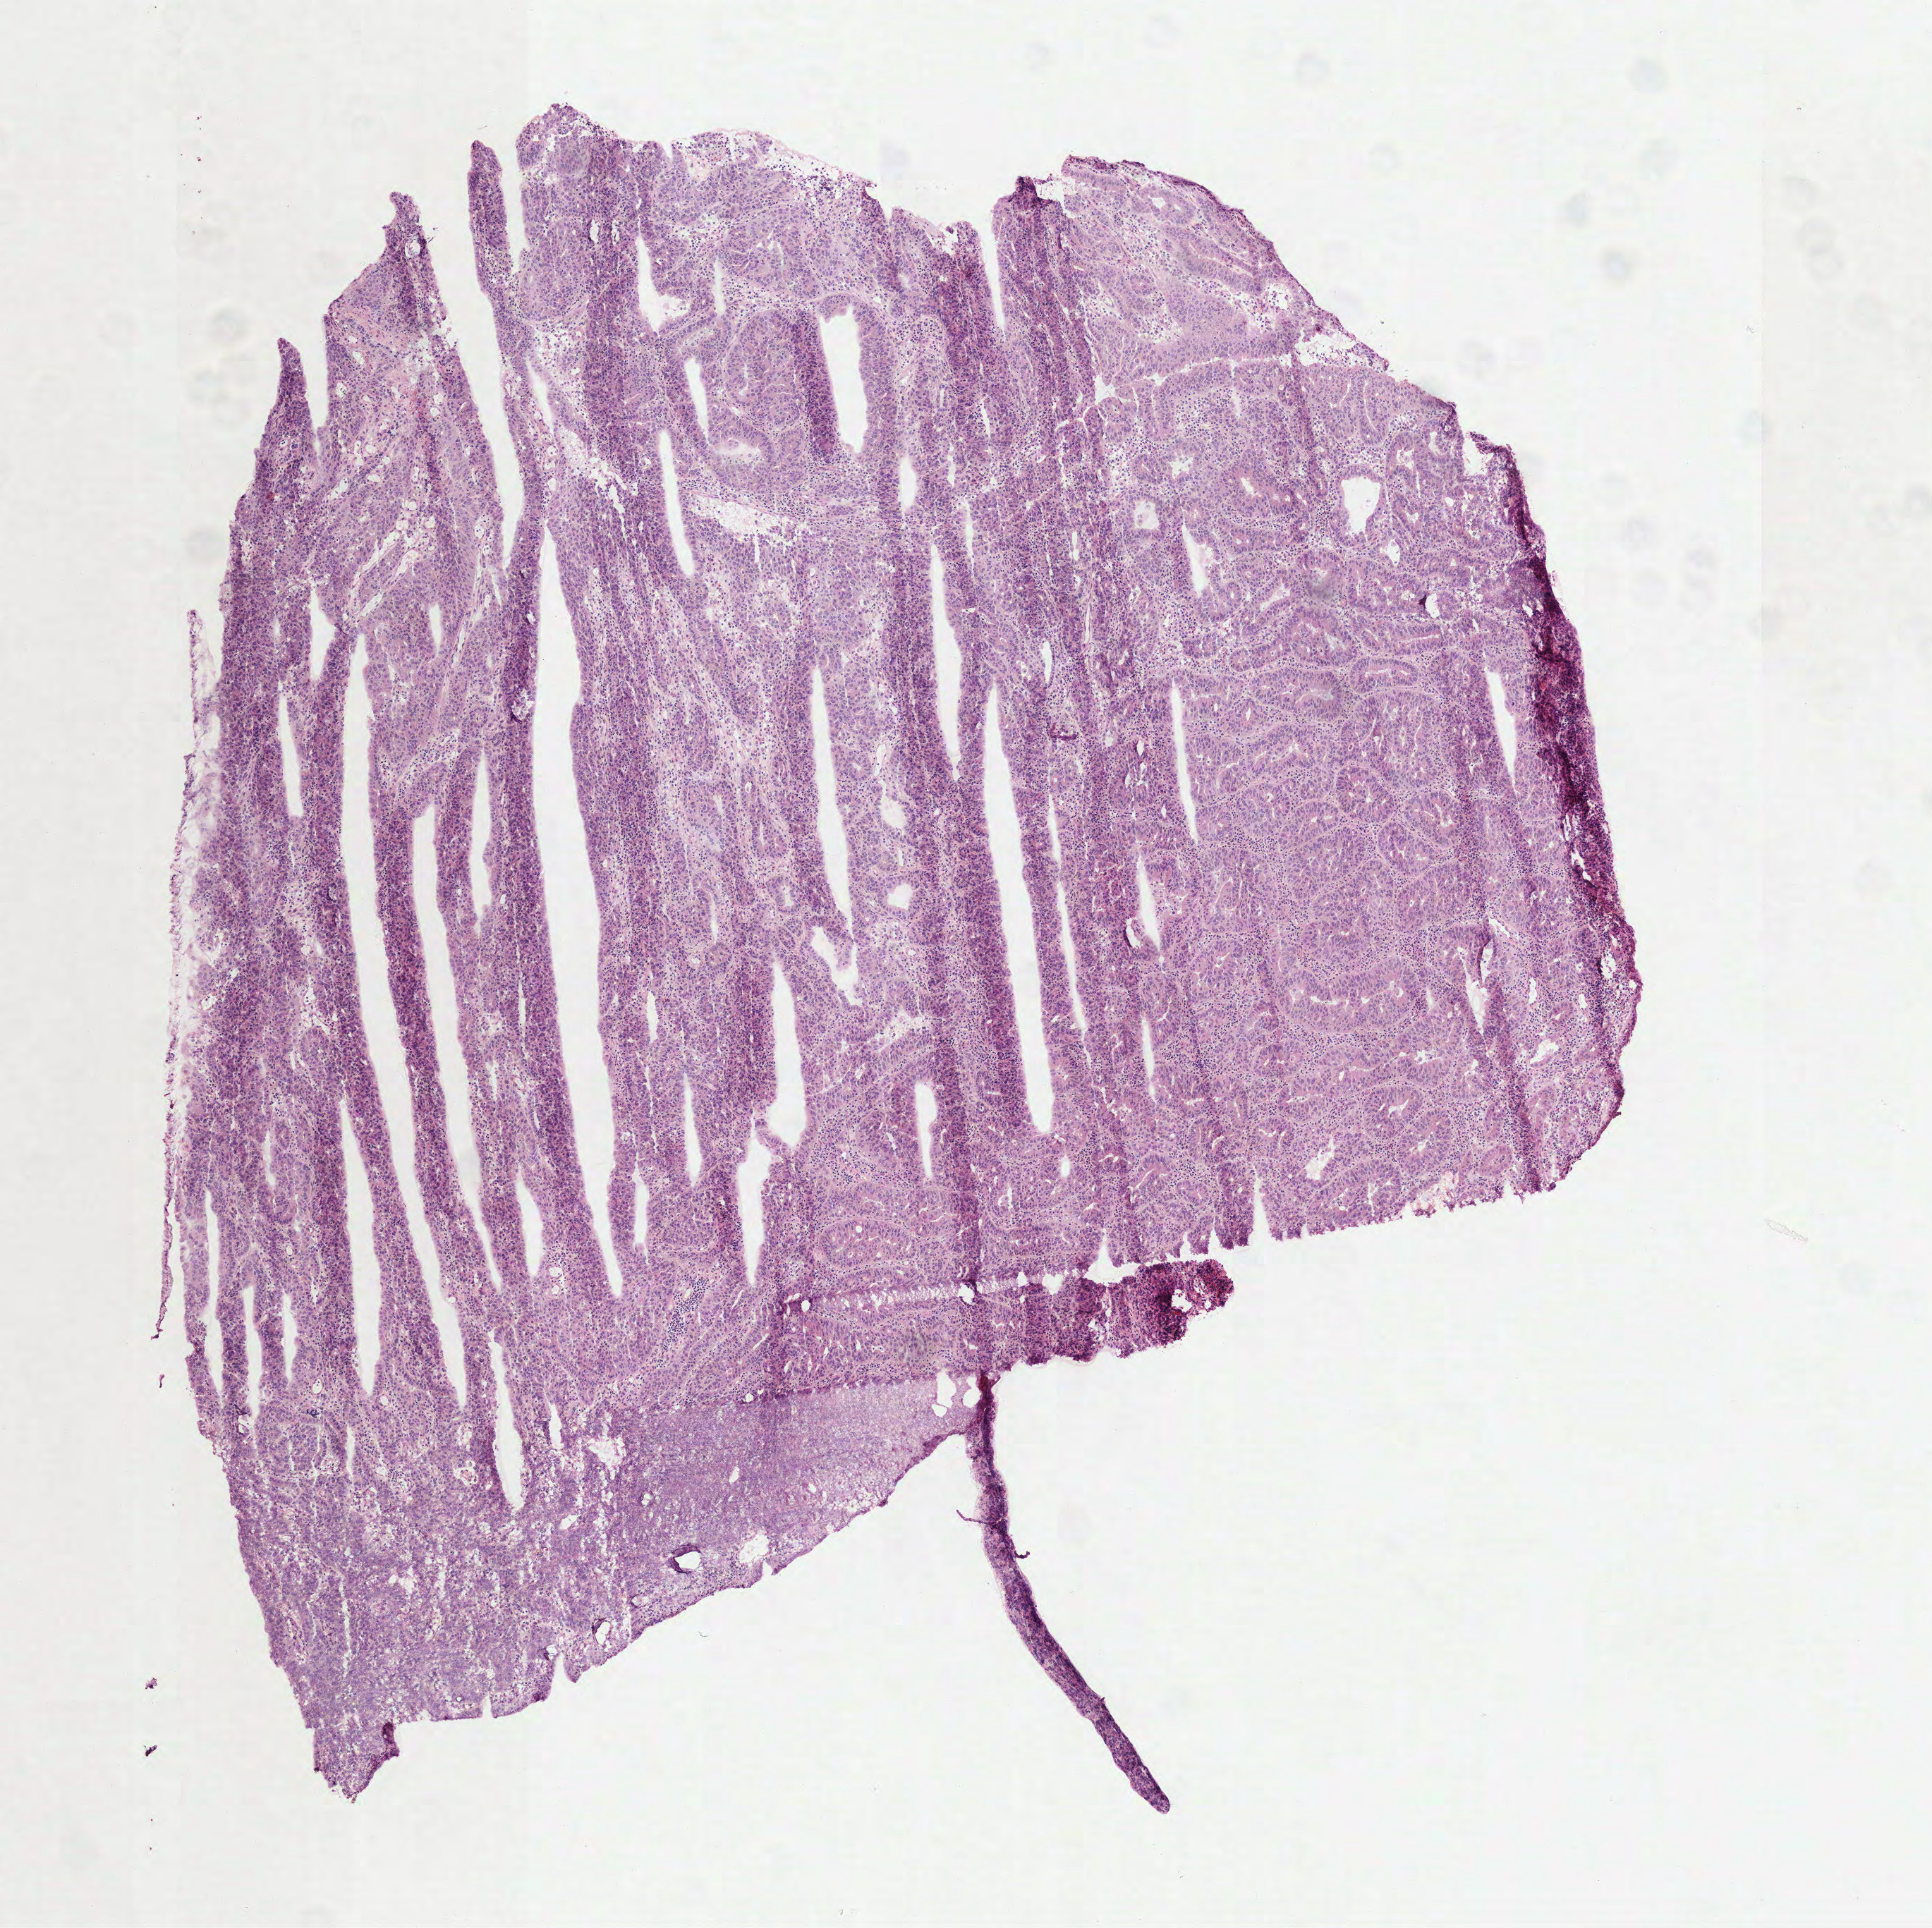
Digitized H&E-stained tissue section (whole slide), shown as a low-resolution overview of the whole scanned area (about 5.5 x 5.5 mm, from a 40x scan), frozen section from the top of the tissue portion, primary tumour sample from the stomach. Patient: male, age at initial diagnosis 44 years. Histologic grade: G3 (poorly differentiated). Pathologist review of this section (percent, as recorded): tumour cells 100%, tumour nuclei 78%, normal cells 0%, stromal cells 0%, necrosis 0%. Infiltration values recorded for this section: lymphocyte infiltration 15%, monocyte infiltration 0%, neutrophil infiltration 0%.
Lymph nodes positive (case pathology): 13 of 24 examined. AJCC pathologic stage: IIIB (7th edition). Pathologic diagnosis: Tubular adenocarcinoma.